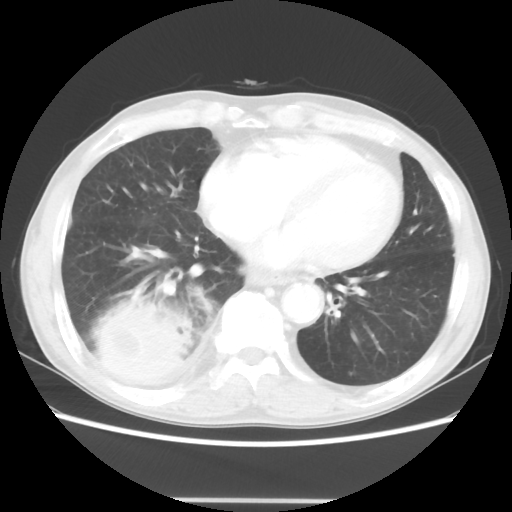
Chest CT, one axial slice; 100 kVp; lung window (W 1500 / L -600 HU); 5 mm slice thickness; 512 × 512 image matrix, field of view 361 × 361 mm. Patient: male, 66 years. Case-level facts recorded for this patient, not image findings: clinical TNM (as recorded): T4 N1 M1; histopathological grade: G3.
Annotated regions visible in this slice (bounding box drawn by a radiologist):
- lung tumour (recorded histology: small cell carcinoma): bounding box <89,300,195,399> (left, top, right, bottom; pixels)